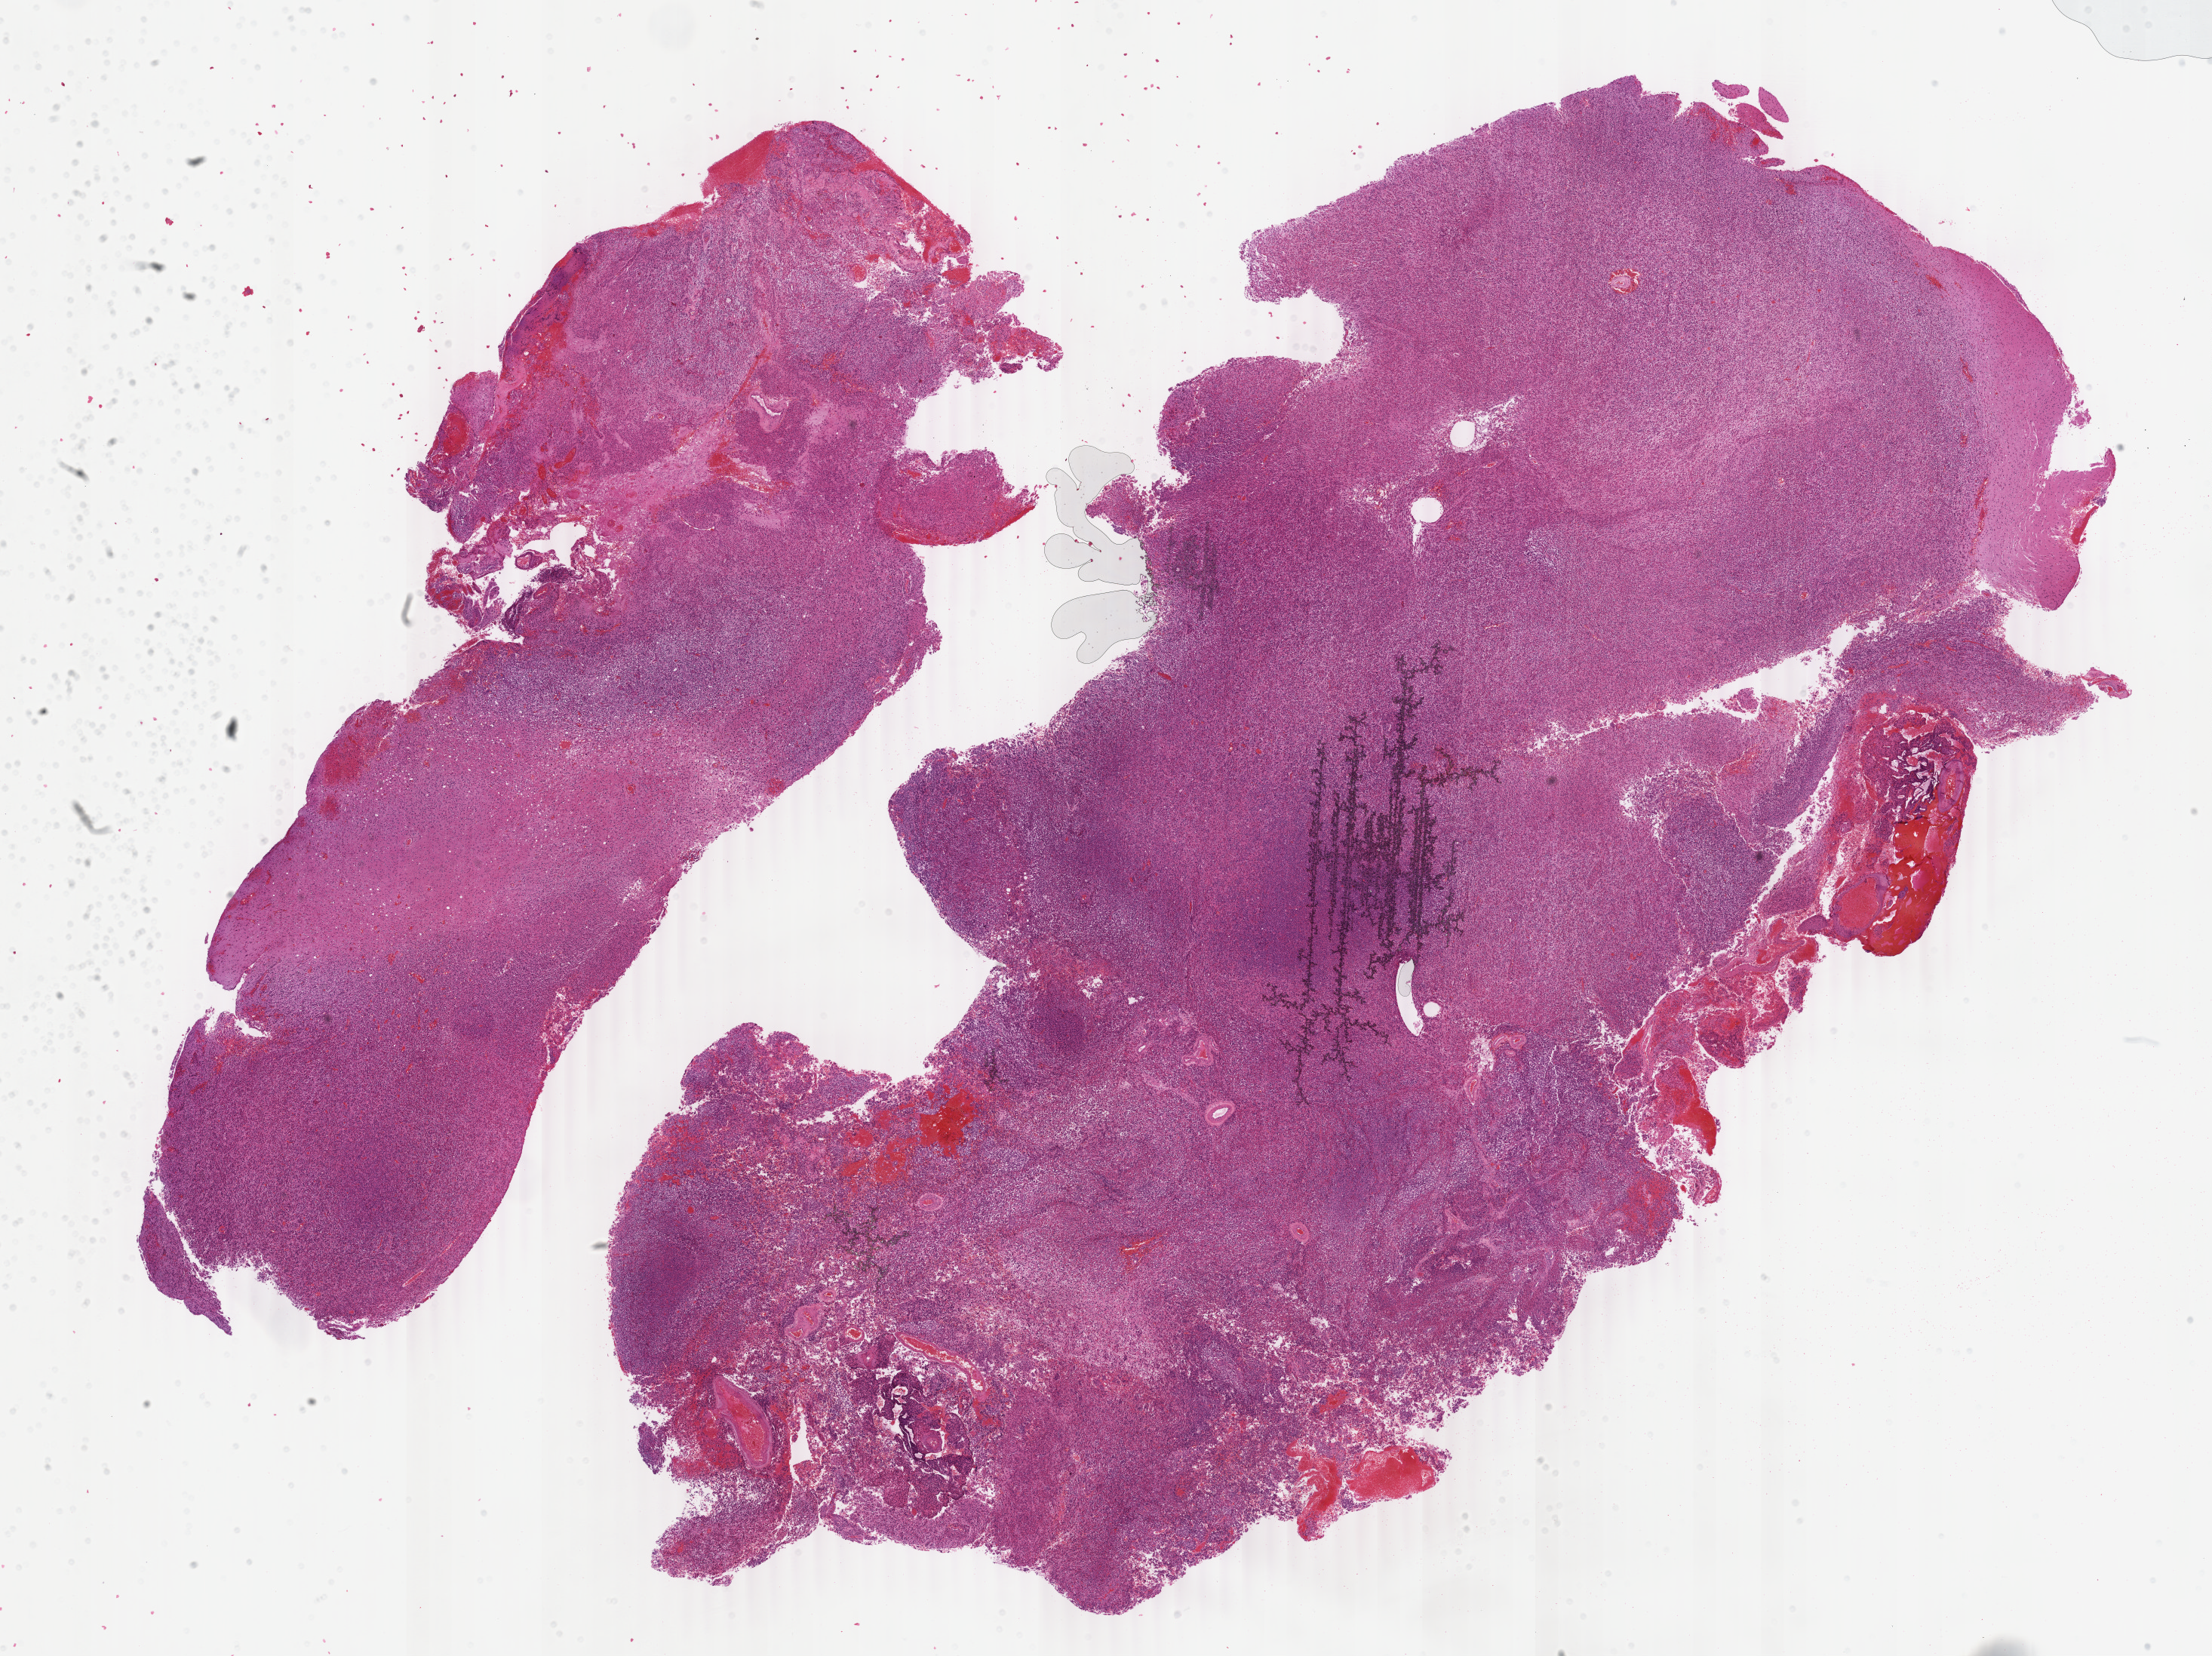
H&E whole-slide image — low-resolution overview of the scanned area, about 23.3 x 17.5 mm (slide scanned at 40x); FFPE section; sample: primary tumour, brain. Male, age 70 years at initial diagnosis. Histologic grade: G3 (poorly differentiated).
Histologic diagnosis: Oligodendroglioma, anaplastic (cerebrum).